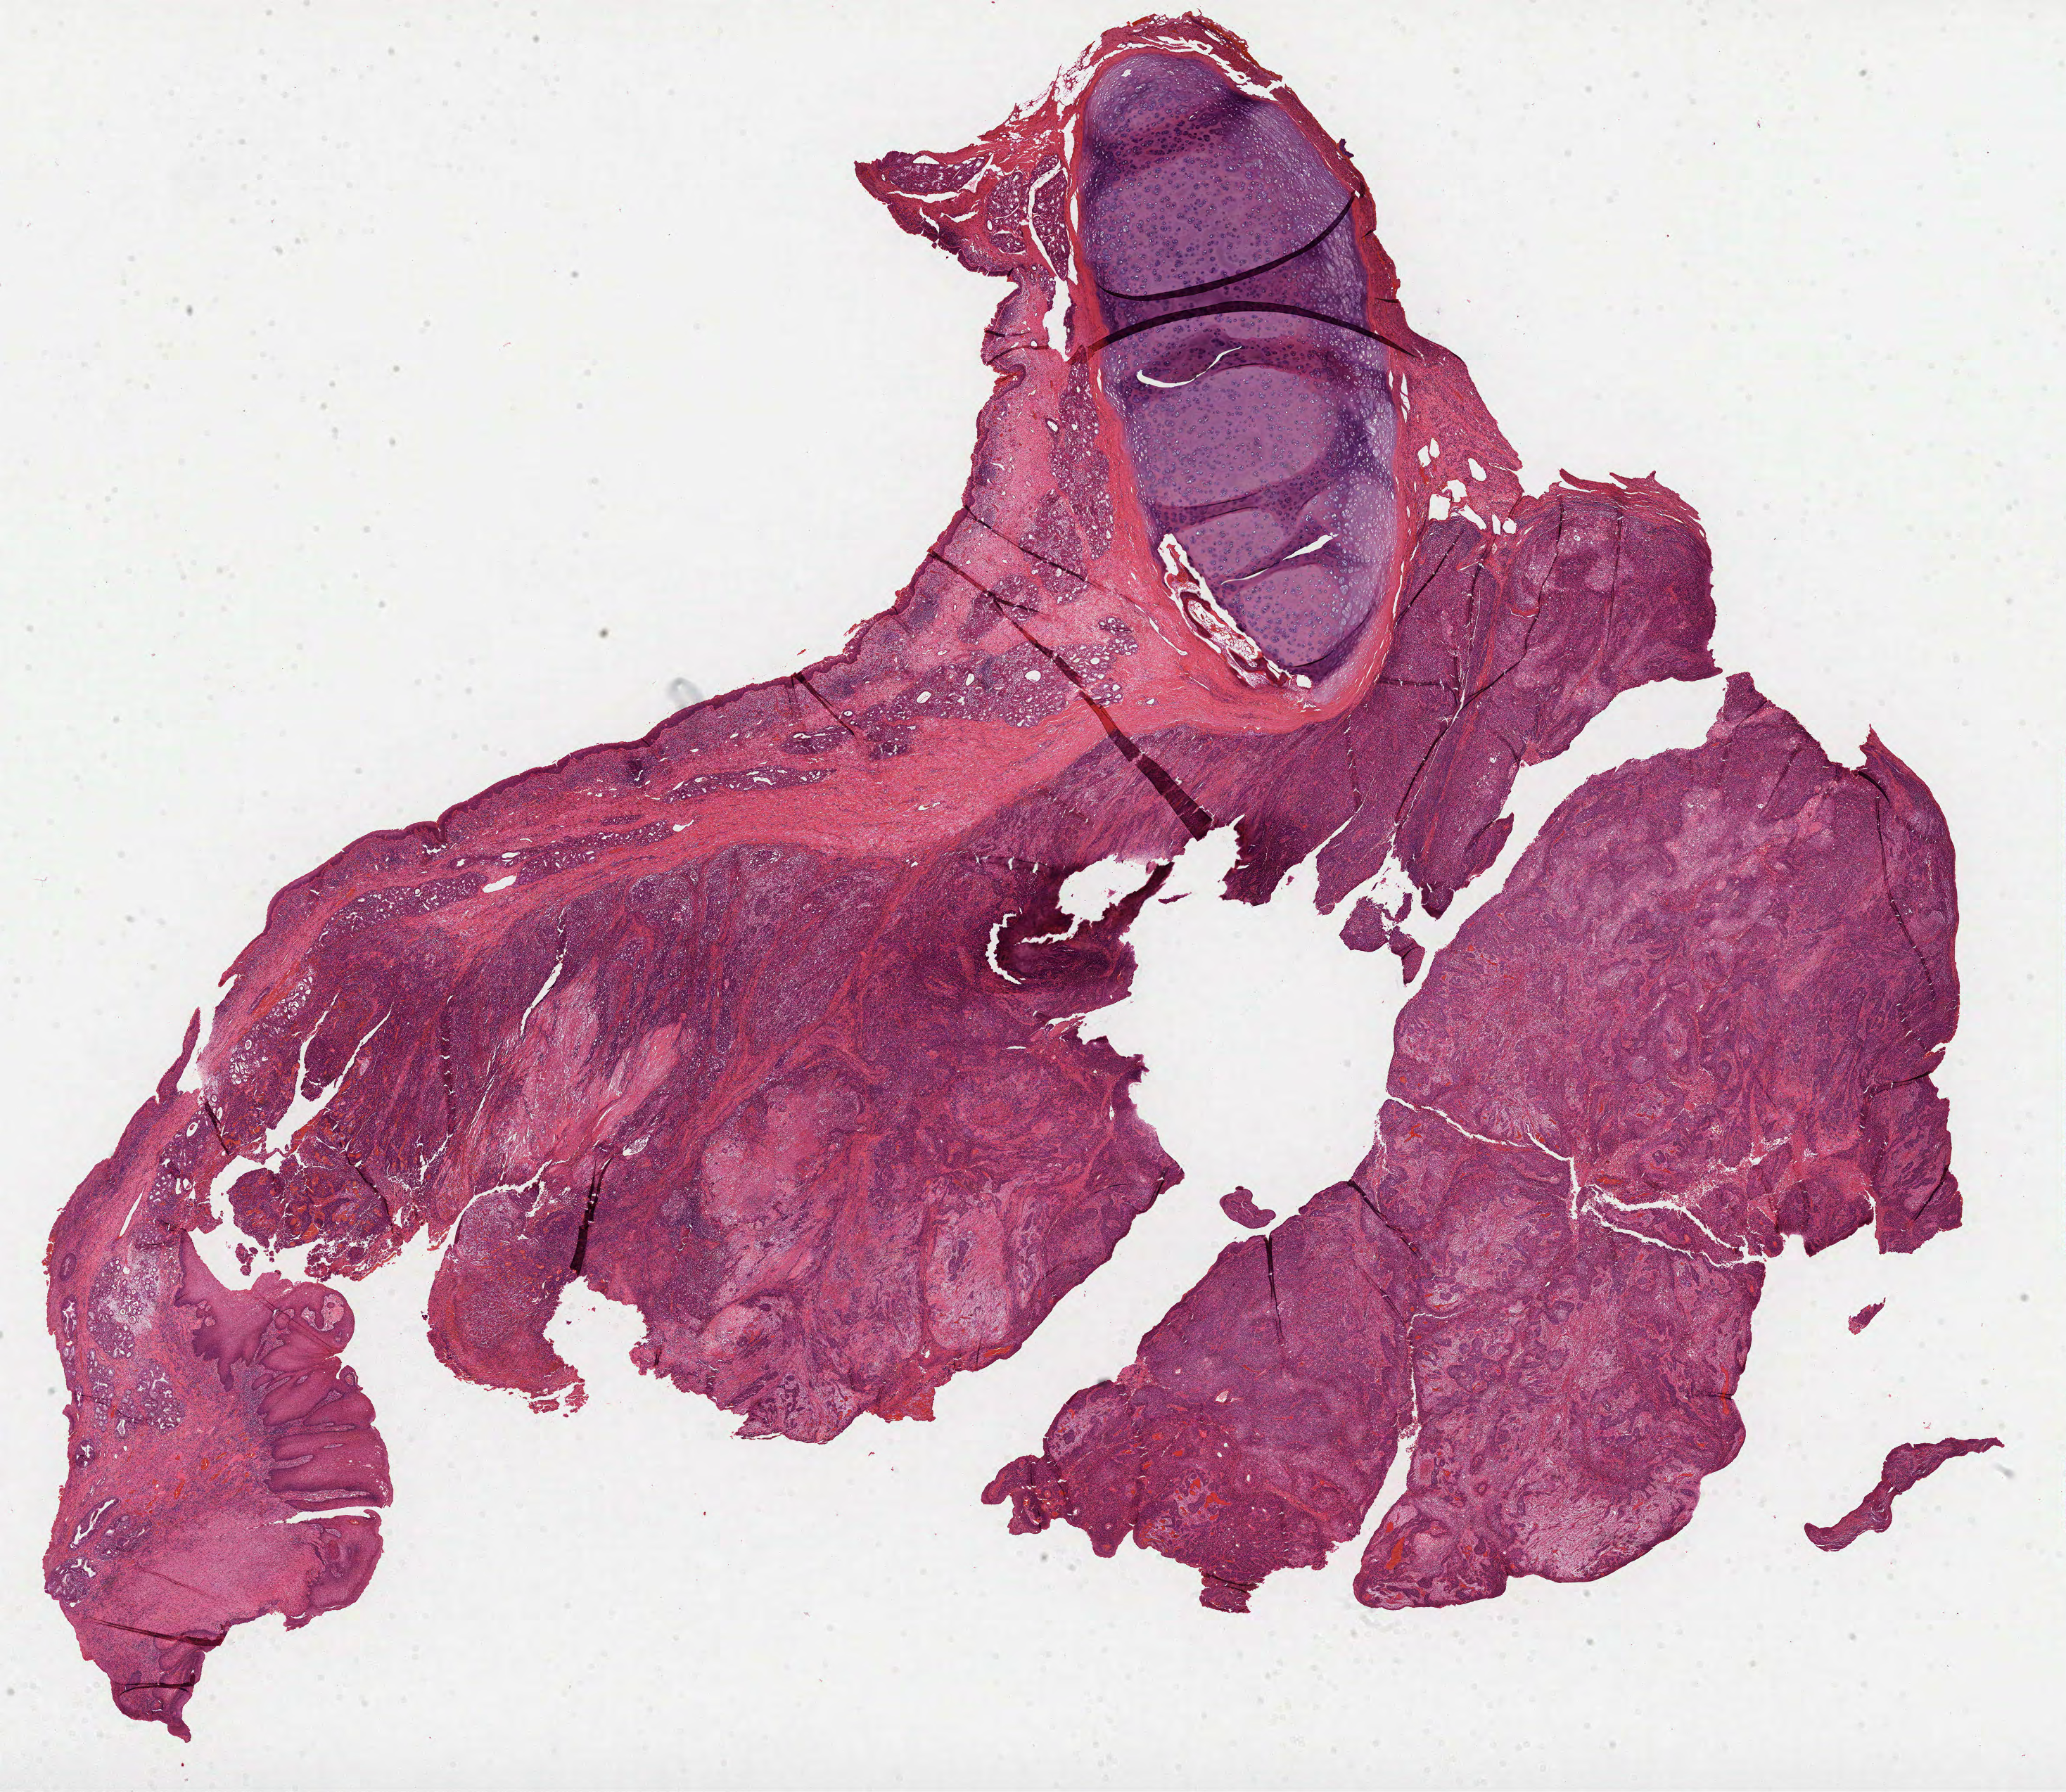
Whole-slide histology image, H&E — shown as a low-resolution overview of the whole scanned area (about 23.7 x 20.6 mm, acquisition: 40x scan). FFPE section. Primary tumour sample from the head and neck. Male patient; age at initial diagnosis 67 years. Histologic grade: G2 (moderately differentiated).
Diagnosis: Squamous cell carcinoma, NOS (larynx, NOS). AJCC pathologic stage: IVA (7th edition).